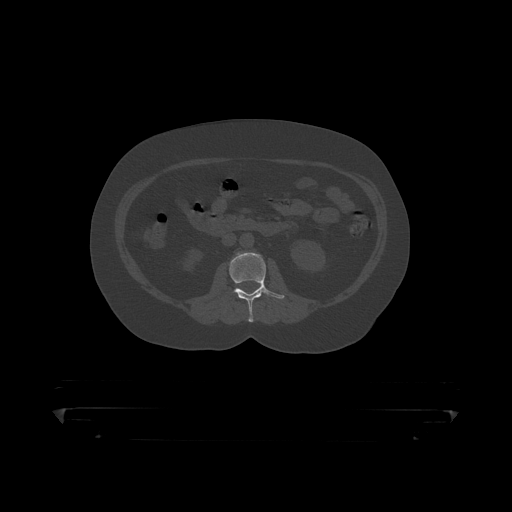
CT including the spine, one axial slice. Slice 114 of 390 in the series (ordered by position). Reconstruction kernel STANDARD. Bone window (W 1800 / L 400 HU). 512 × 512 image matrix. Patient: male, 60 years. Case-level facts recorded for this patient, not image findings: primary cancer: prostate.
Annotated regions visible in this slice (semi-automatic segmentation, software-assisted and operator-edited):
- L2 vertebra: bounding box (x1, y1, x2, y2) in pixels: (229, 253, 285, 319)